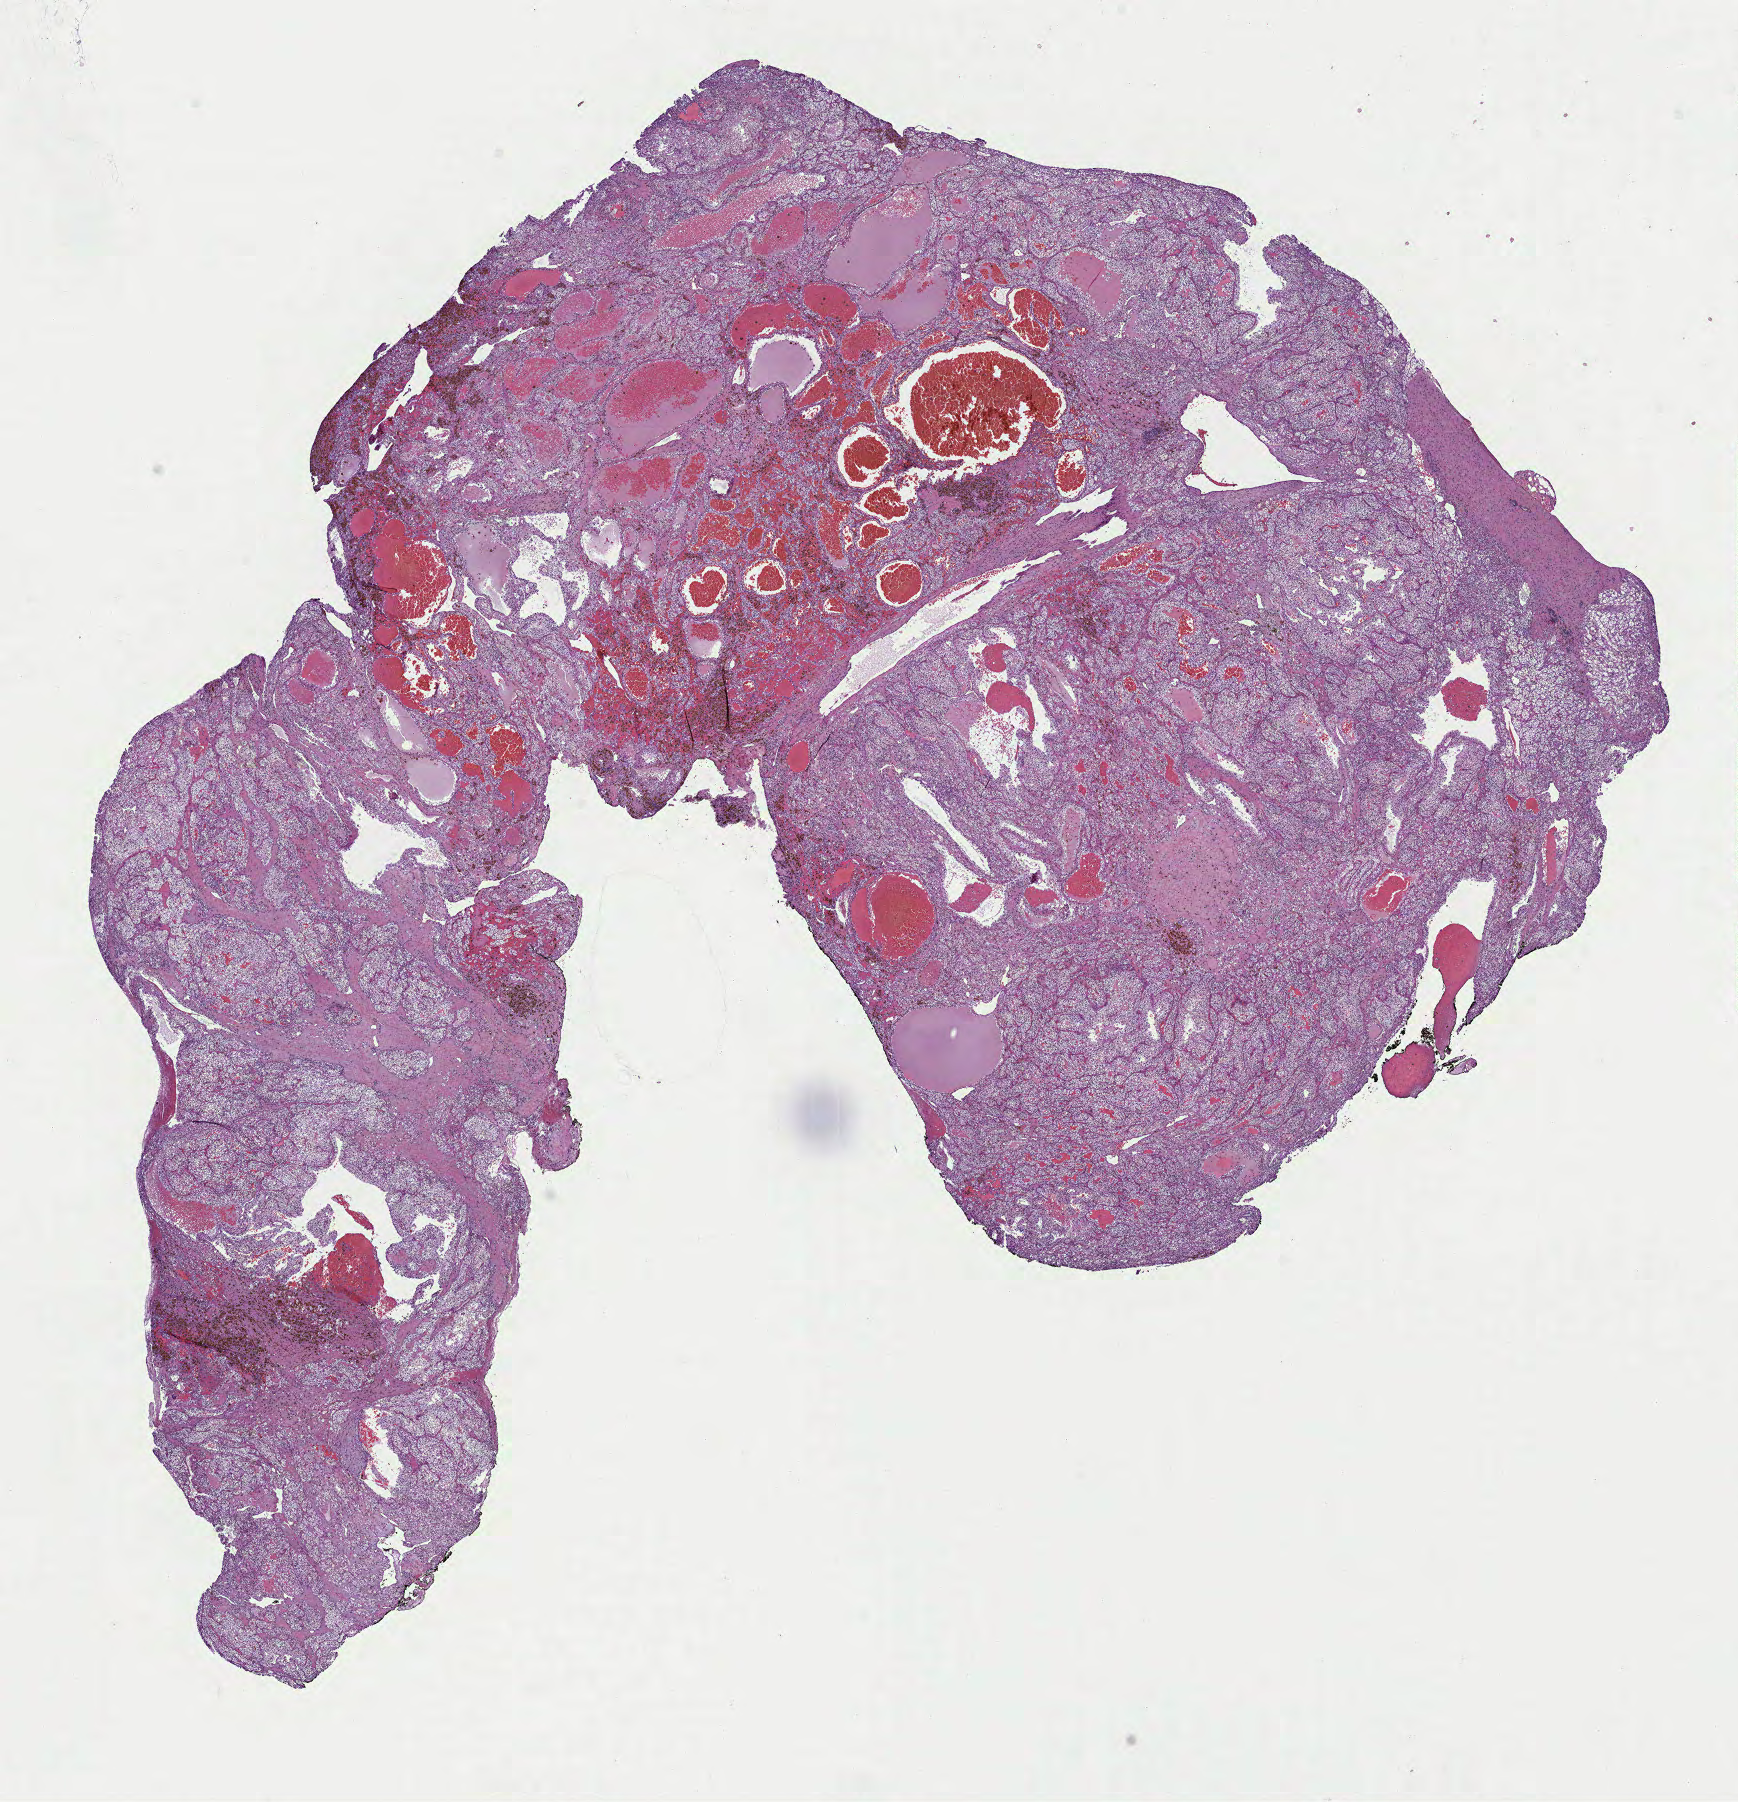
H&E-stained whole-slide image — whole scanned area (about 14.0 x 14.5 mm) shown as a low-resolution overview; formalin-fixed paraffin-embedded (FFPE) diagnostic section; primary tumour sample from the kidney. Male, age 47 years at initial diagnosis.
Histologic diagnosis: Renal cell carcinoma, NOS.